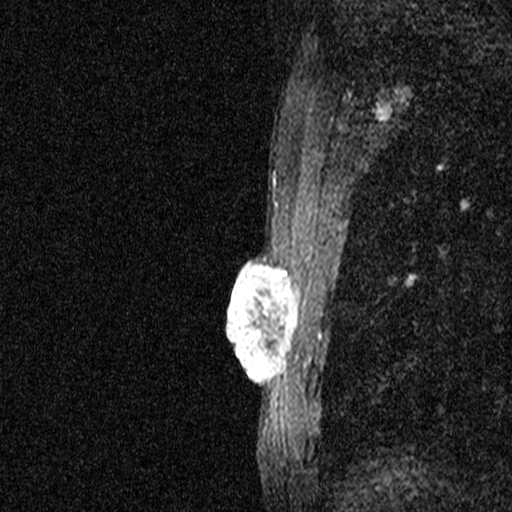
Breast MRI (dynamic contrast-enhanced), one sagittal slice. Position 35 of 44 along the scan axis. Dynamic contrast-enhanced study with each time point stored as its own series, time point 2 of 3 at this slice position (early post-contrast, ordered by acquisition time). 1.5 T. TE 4.5 ms, TR 11 ms. 2.05 mm slice thickness. 512 × 512 image matrix. Female patient, age 44 years. From the clinical record (not read from this slice): setting: breast cancer imaged before/during neoadjuvant chemotherapy; receptor status: HR-positive, HER2-negative.
Outlined on this slice (semi-automatically segmented with operator editing):
- analysis volume of interest (the breast-tissue region the enhancement analysis was run in; not a lesion): bounding box <204,254,307,401> (left, top, right, bottom; pixels)
- tumour enhancement mask (voxels above the 90 % enhancement threshold inside the analysis volume of interest): <228,261,304,401>